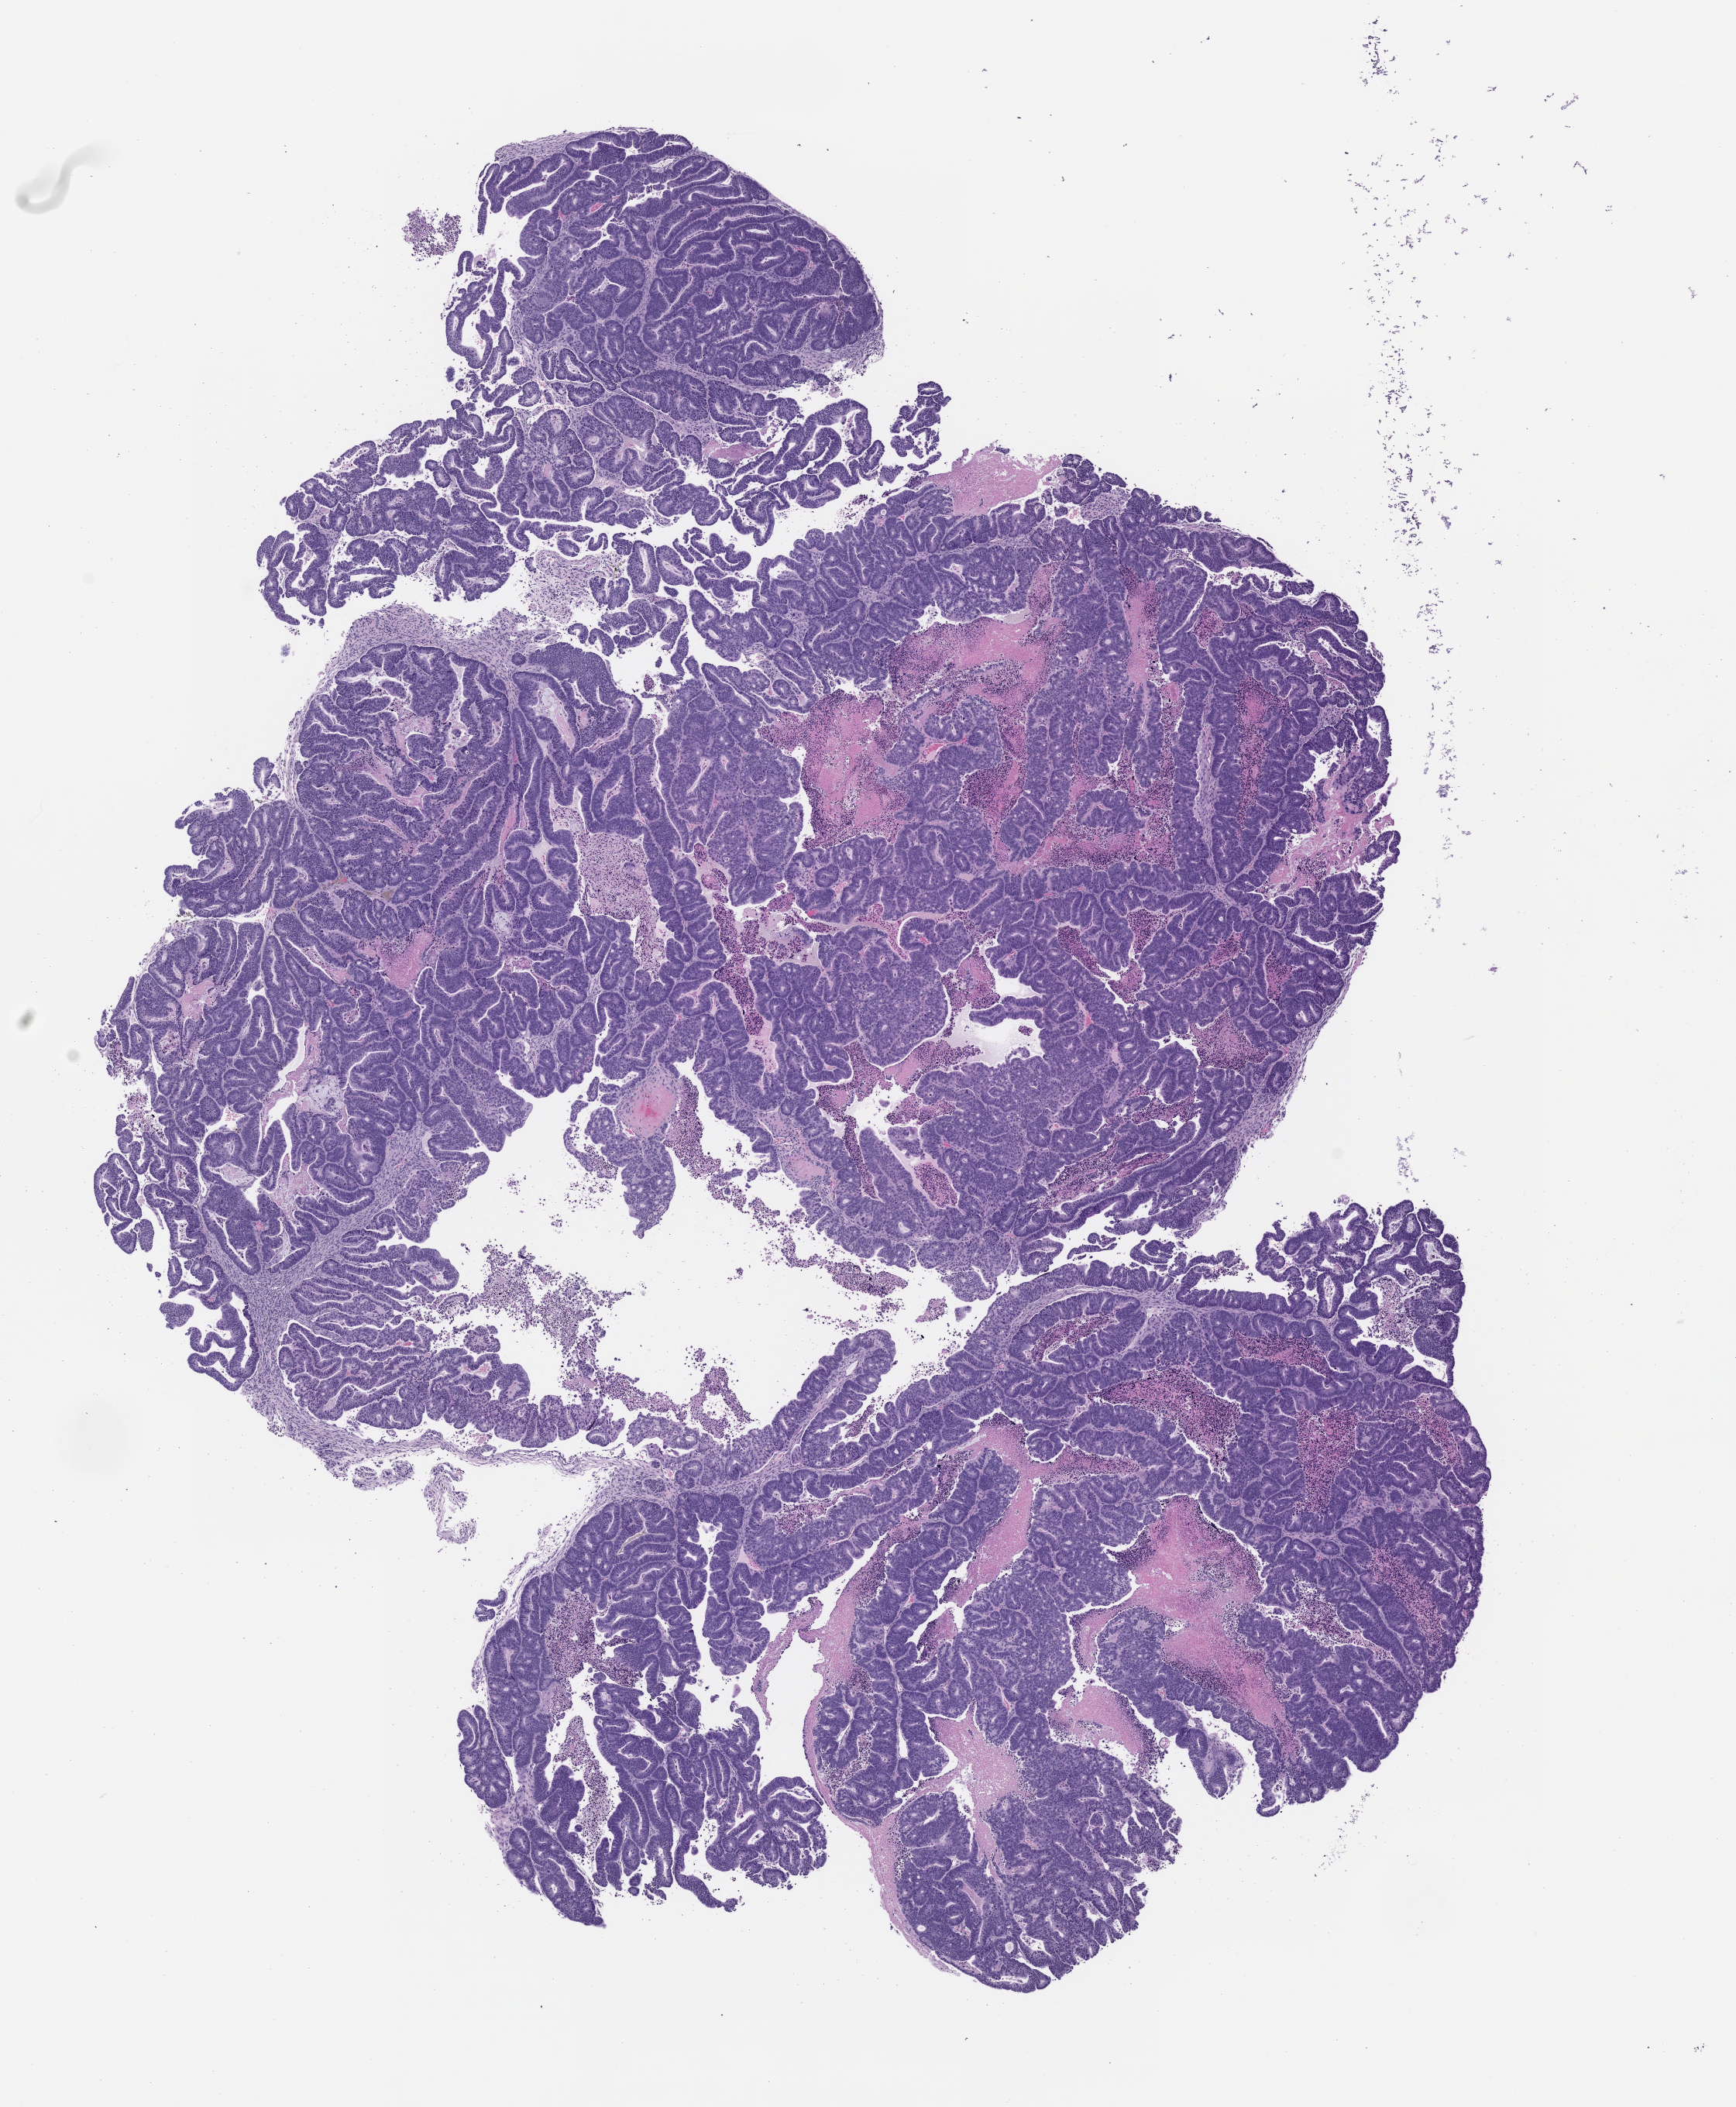
Hematoxylin and eosin (H&E) whole-slide image of a patient-derived xenograft (PDX) tumor grown in a mouse, passage 1 — whole scanned area (about 9.0 x 10.9 mm) shown as a low-resolution overview, formalin-fixed, paraffin-embedded (FFPE) tissue, originating tumor site category: colon.
Originating patient diagnosis: Colon Adenocarcinoma.